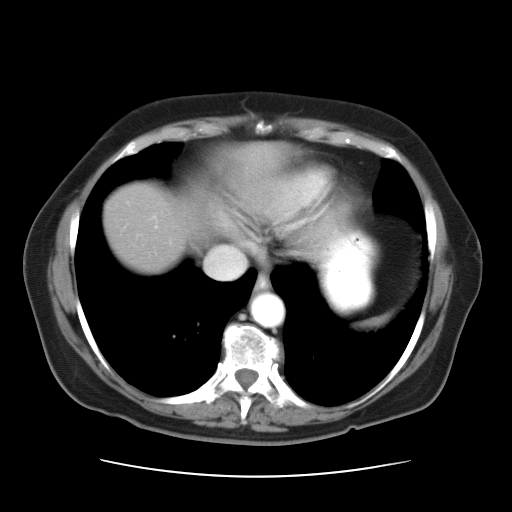
Contrast-enhanced abdominal CT, one axial slice; position 30 of 34 along the scan axis; 120 kVp; intravenous contrast given; soft-tissue window (W 400 / L 40 HU); 7.5 mm slice thickness; 512 × 512 image matrix. Female patient, age 65 years. Case-level facts recorded for this patient, not image findings: diagnosis: colorectal cancer liver metastases, imaged before liver resection; multiple liver metastases: yes; largest metastasis: 2.2 cm.
Annotated regions visible in this slice (outlined manually by an expert reader):
- hepatic veins: bounding box (x1, y1, x2, y2) in pixels: (207, 247, 244, 279)
- liver: (107, 187, 188, 265)
- planned liver remnant (the part of the liver to remain after resection): (107, 187, 188, 266)